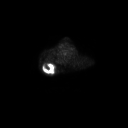
FDG PET of an extremity soft-tissue mass (from a PET/CT study), one axial slice. Slice 219 of 267 in the series (ordered by position). 3.27 mm slice thickness. 128 × 128 image matrix, field of view 700 × 700 mm. Patient: male, 61 years. From the clinical record (not read from this slice): histological type: pleiomorphic spindle cell undifferentiated; grade: high; site of the primary tumour: right parascapusular.
Annotated regions visible in this slice (expert contour drawn on MRI and transferred to this co-registered scan by the dataset authors):
- gross tumour volume including surrounding oedema: bounding box <42,64,56,73> (left, top, right, bottom; pixels)
- gross tumour volume (mass): <42,64,52,72>